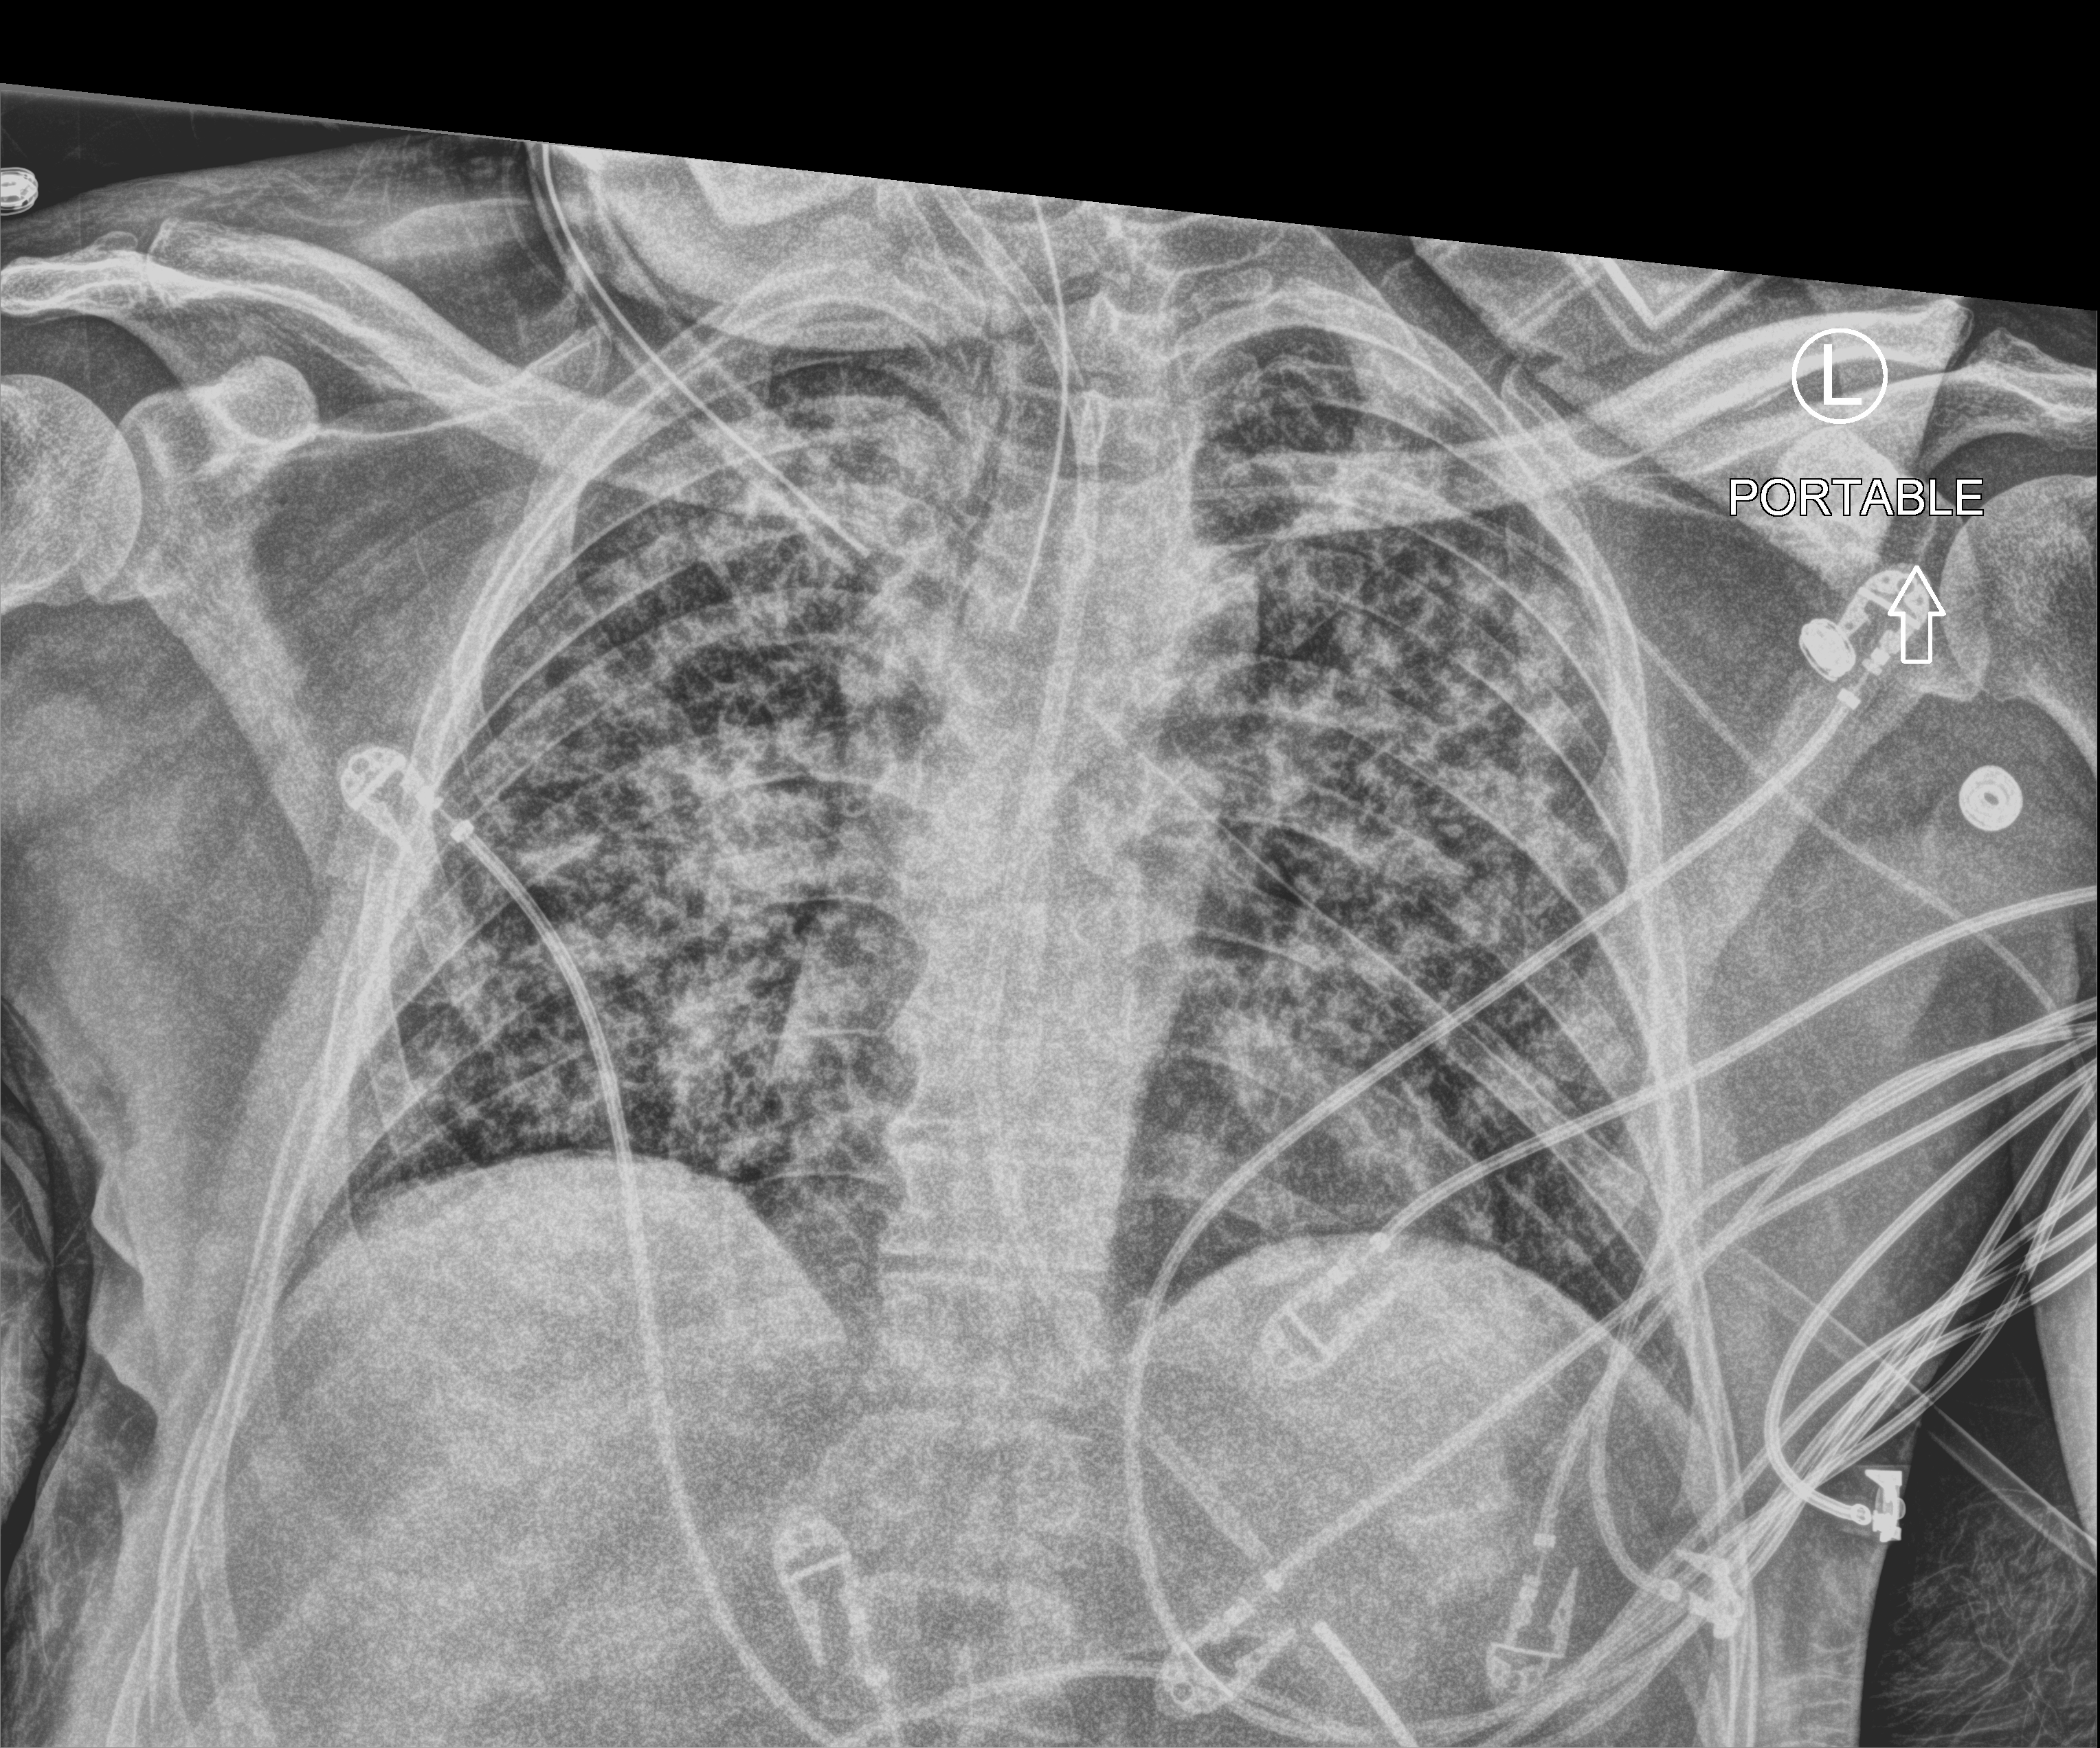
Portable chest radiograph; anteroposterior (AP) projection. Male patient hospitalised with COVID-19, age 18–59 years.
From the hospital-stay record, not from the radiograph (when in the stay this image was taken is not recorded):
- admitted to intensive care during this hospital stay: yes
- COPD (admission record): no
- hypertension (admission record): yes